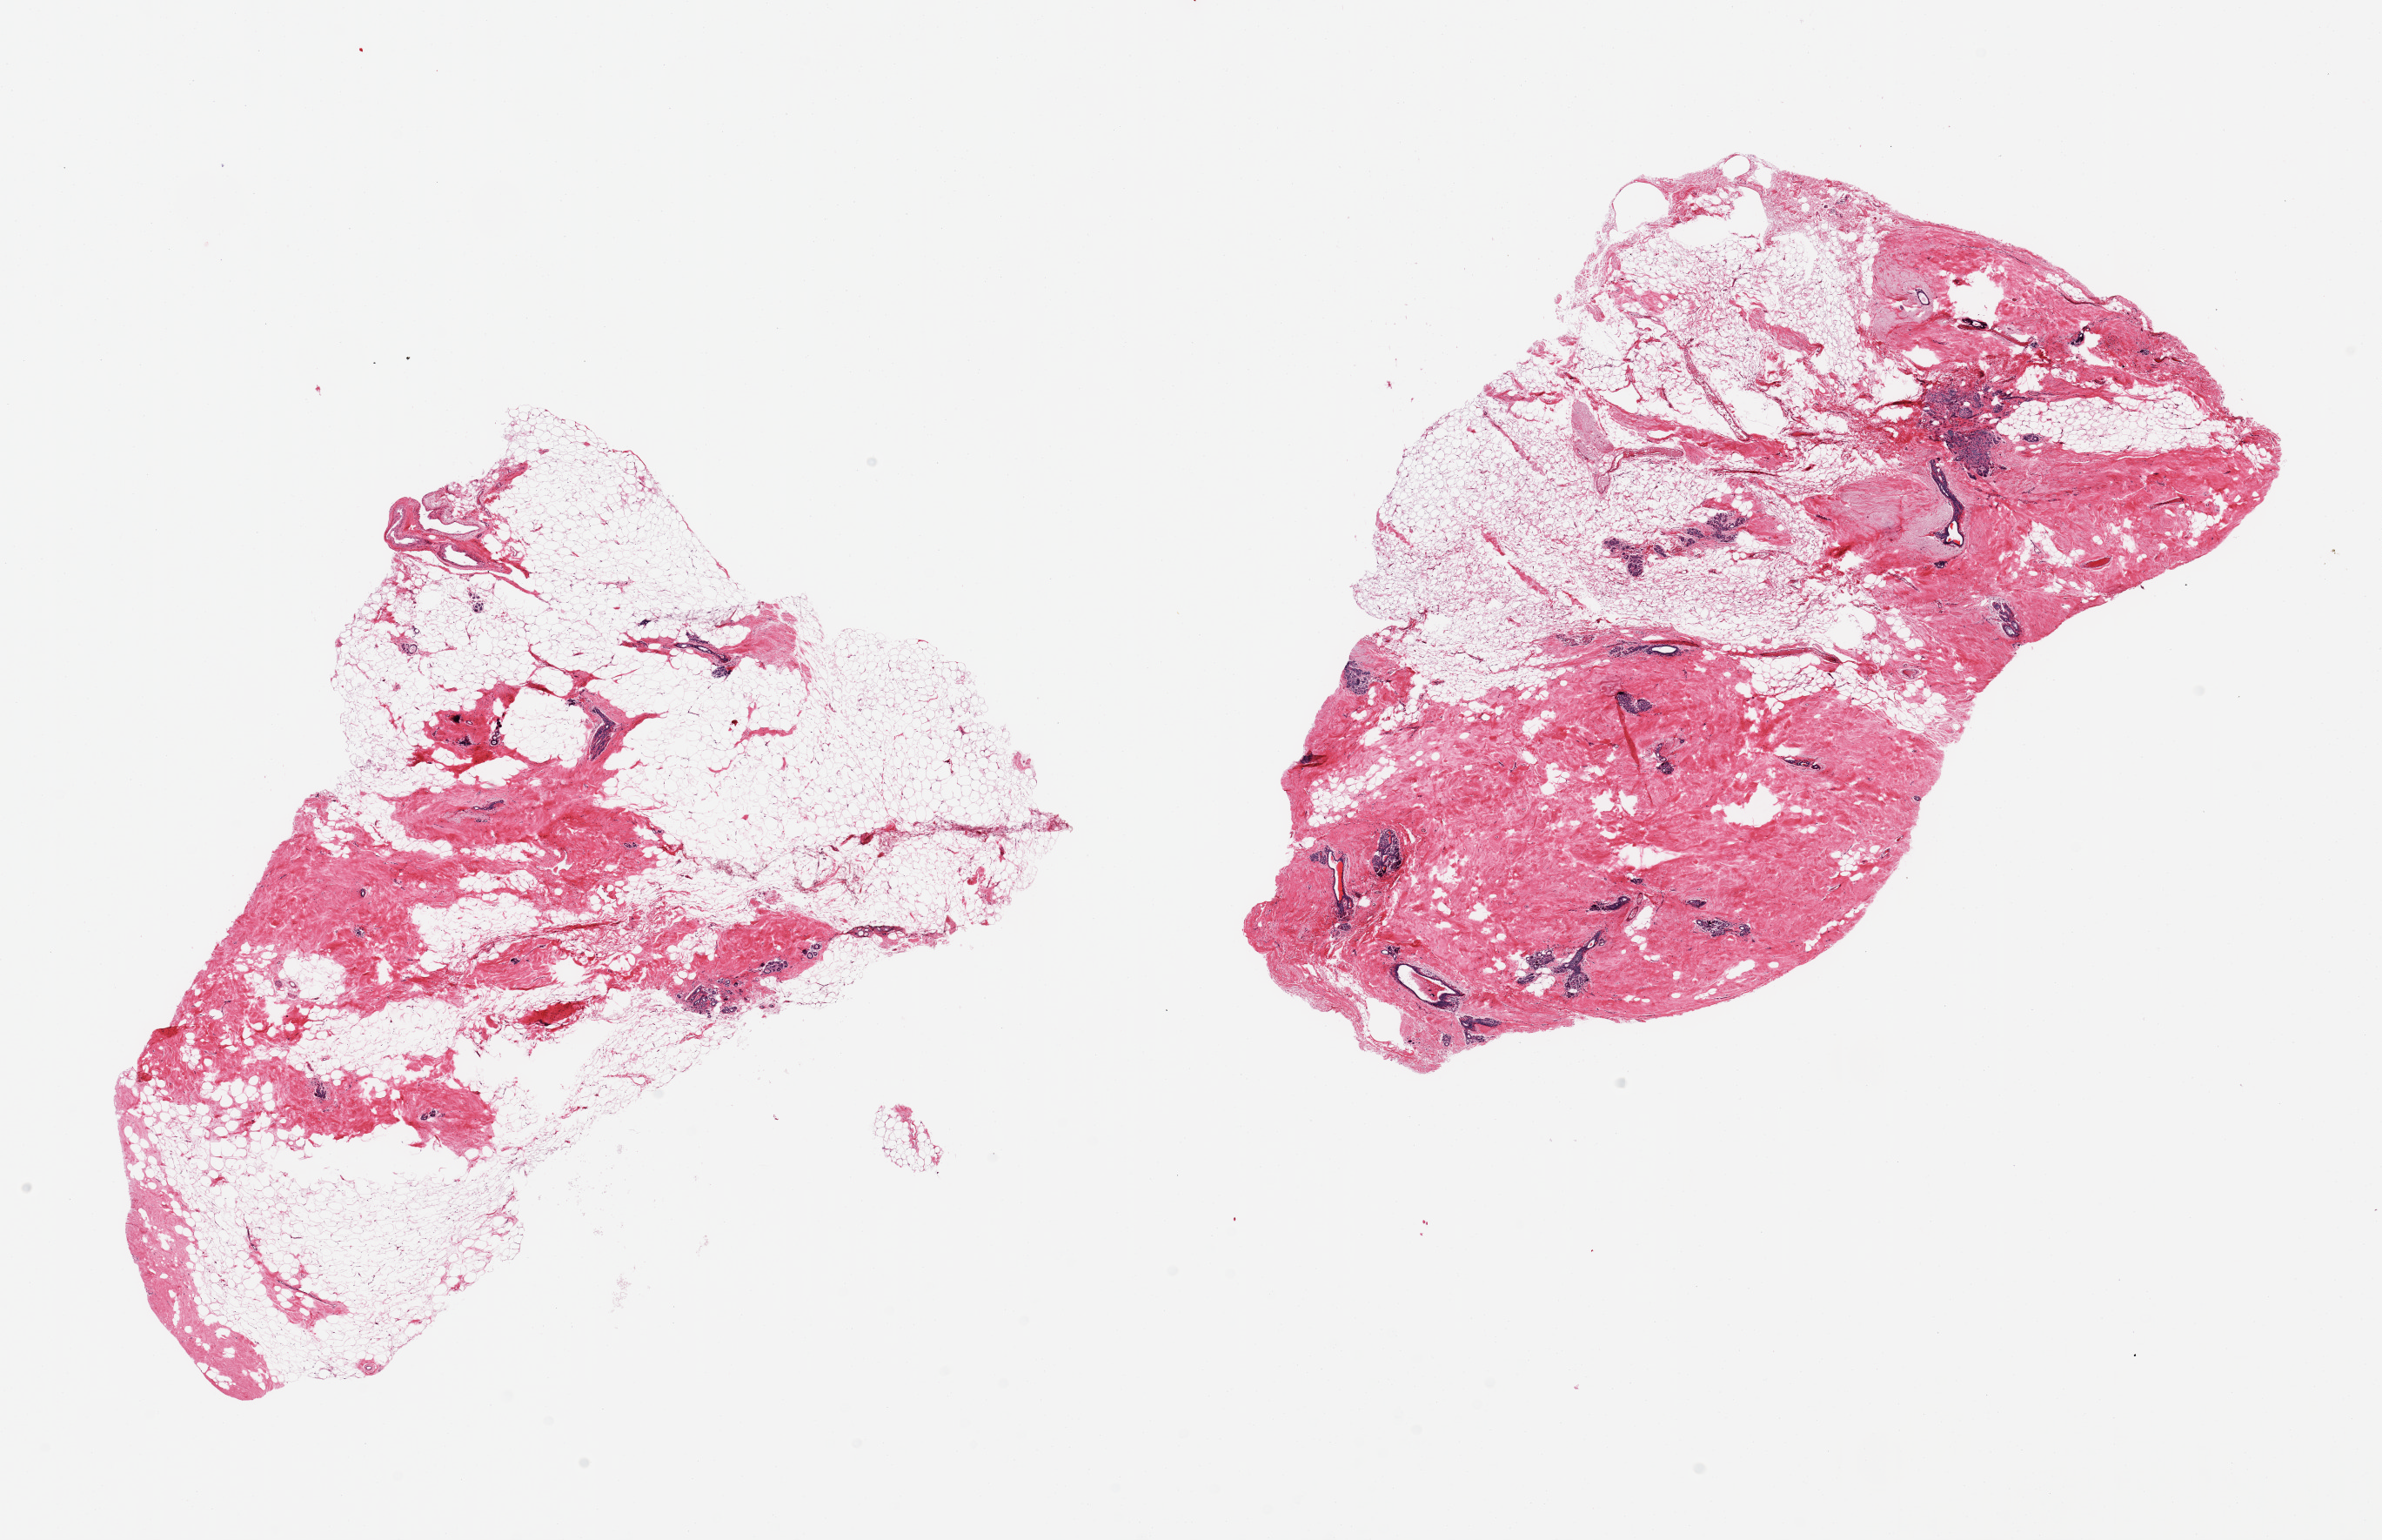
Digitized H&E-stained section, a low-resolution overview of the entire scanned area, about 21.7 x 14.0 mm, PAXgene-fixed, paraffin-embedded tissue, sampled site (target tissue): breast, tissue donor sample. Donor: female.
Pathologist's review note for this sample: 2 pieces; 70 and 30% fat with dense stroma and ducts and lobules with focal microcalcification, sclerosing adenosis.